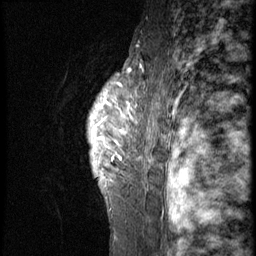
Breast MRI (dynamic contrast-enhanced), one sagittal slice; position 48 of 58 along the scan axis; 3 images stored at this slice position (order not interpretable as contrast timing); 1.5 T; TE 4.2 ms, TR 9 ms; 256 × 256 image matrix. Patient: female, 50 years. From the clinical record (not read from this slice): setting: breast cancer imaged before/during neoadjuvant chemotherapy; receptor status: triple-negative.
Annotated regions visible in this slice (semi-automatic segmentation, software-assisted and operator-edited):
- analysis volume of interest (the breast-tissue region the enhancement analysis was run in; not a lesion): box from (x=64, y=67) to (x=126, y=214) px
- tumour enhancement mask (voxels above the 140 % enhancement threshold inside the analysis volume of interest): (x=89, y=80)–(x=126, y=187)